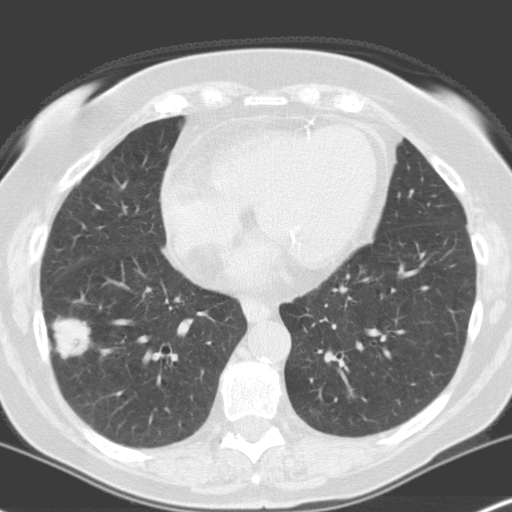
Low-dose screening chest CT, one axial slice; slice 69 of 160 in the series (ordered by position); 120 kVp; lung window (W 1500 / L -600 HU); 3.2 mm slice thickness; 512 × 512 image matrix, field of view 316 × 316 mm.
Structures marked on this image (manually delineated by an expert):
- lesion 1 (tumor, lower lobe of right lung): bounding box (x1, y1, x2, y2) in pixels: (53, 317, 90, 358)